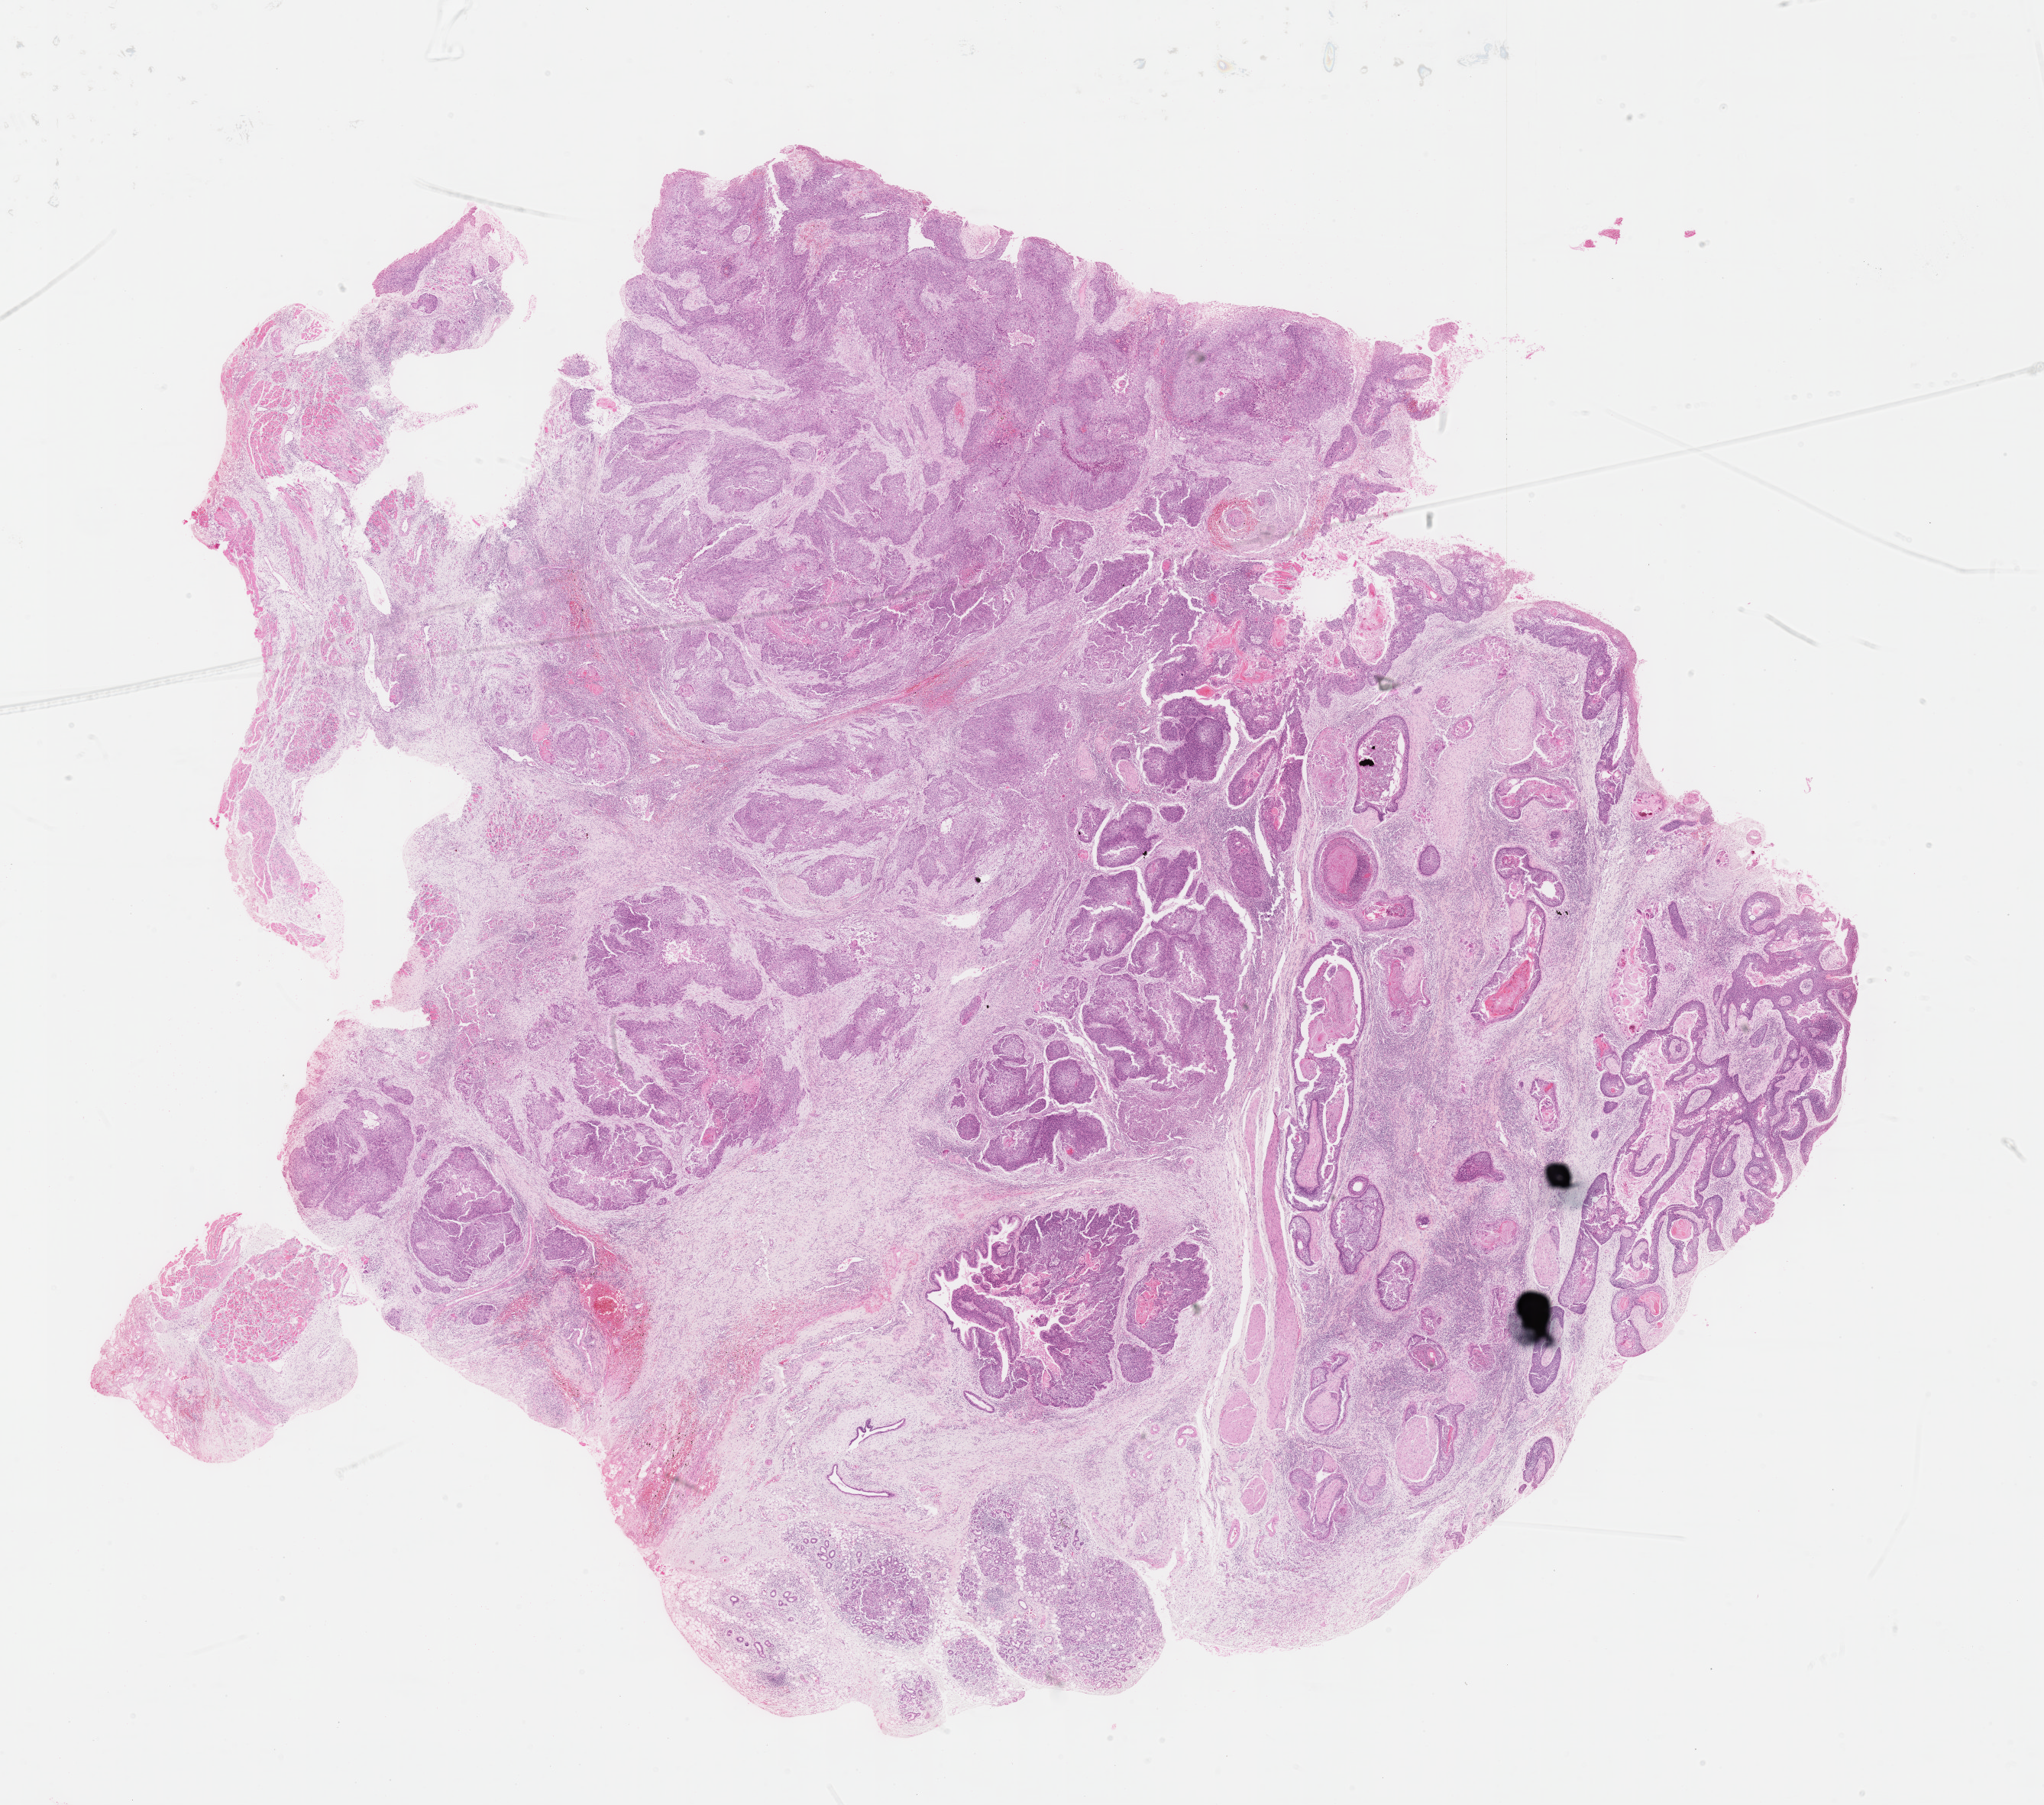
H&E-stained whole-slide image, whole scanned area (about 21.6 x 19.1 mm) shown as a low-resolution overview. Formalin-fixed paraffin-embedded (FFPE) diagnostic section. Sample: primary tumour, head and neck. Female patient; age at initial diagnosis 57 years. Histologic grade: G2 (moderately differentiated).
• diagnosis: Squamous cell carcinoma, NOS (overlapping lesion of lip, oral cavity and pharynx)
• laterality: midline
• AJCC pathologic stage: IVA (7th edition)